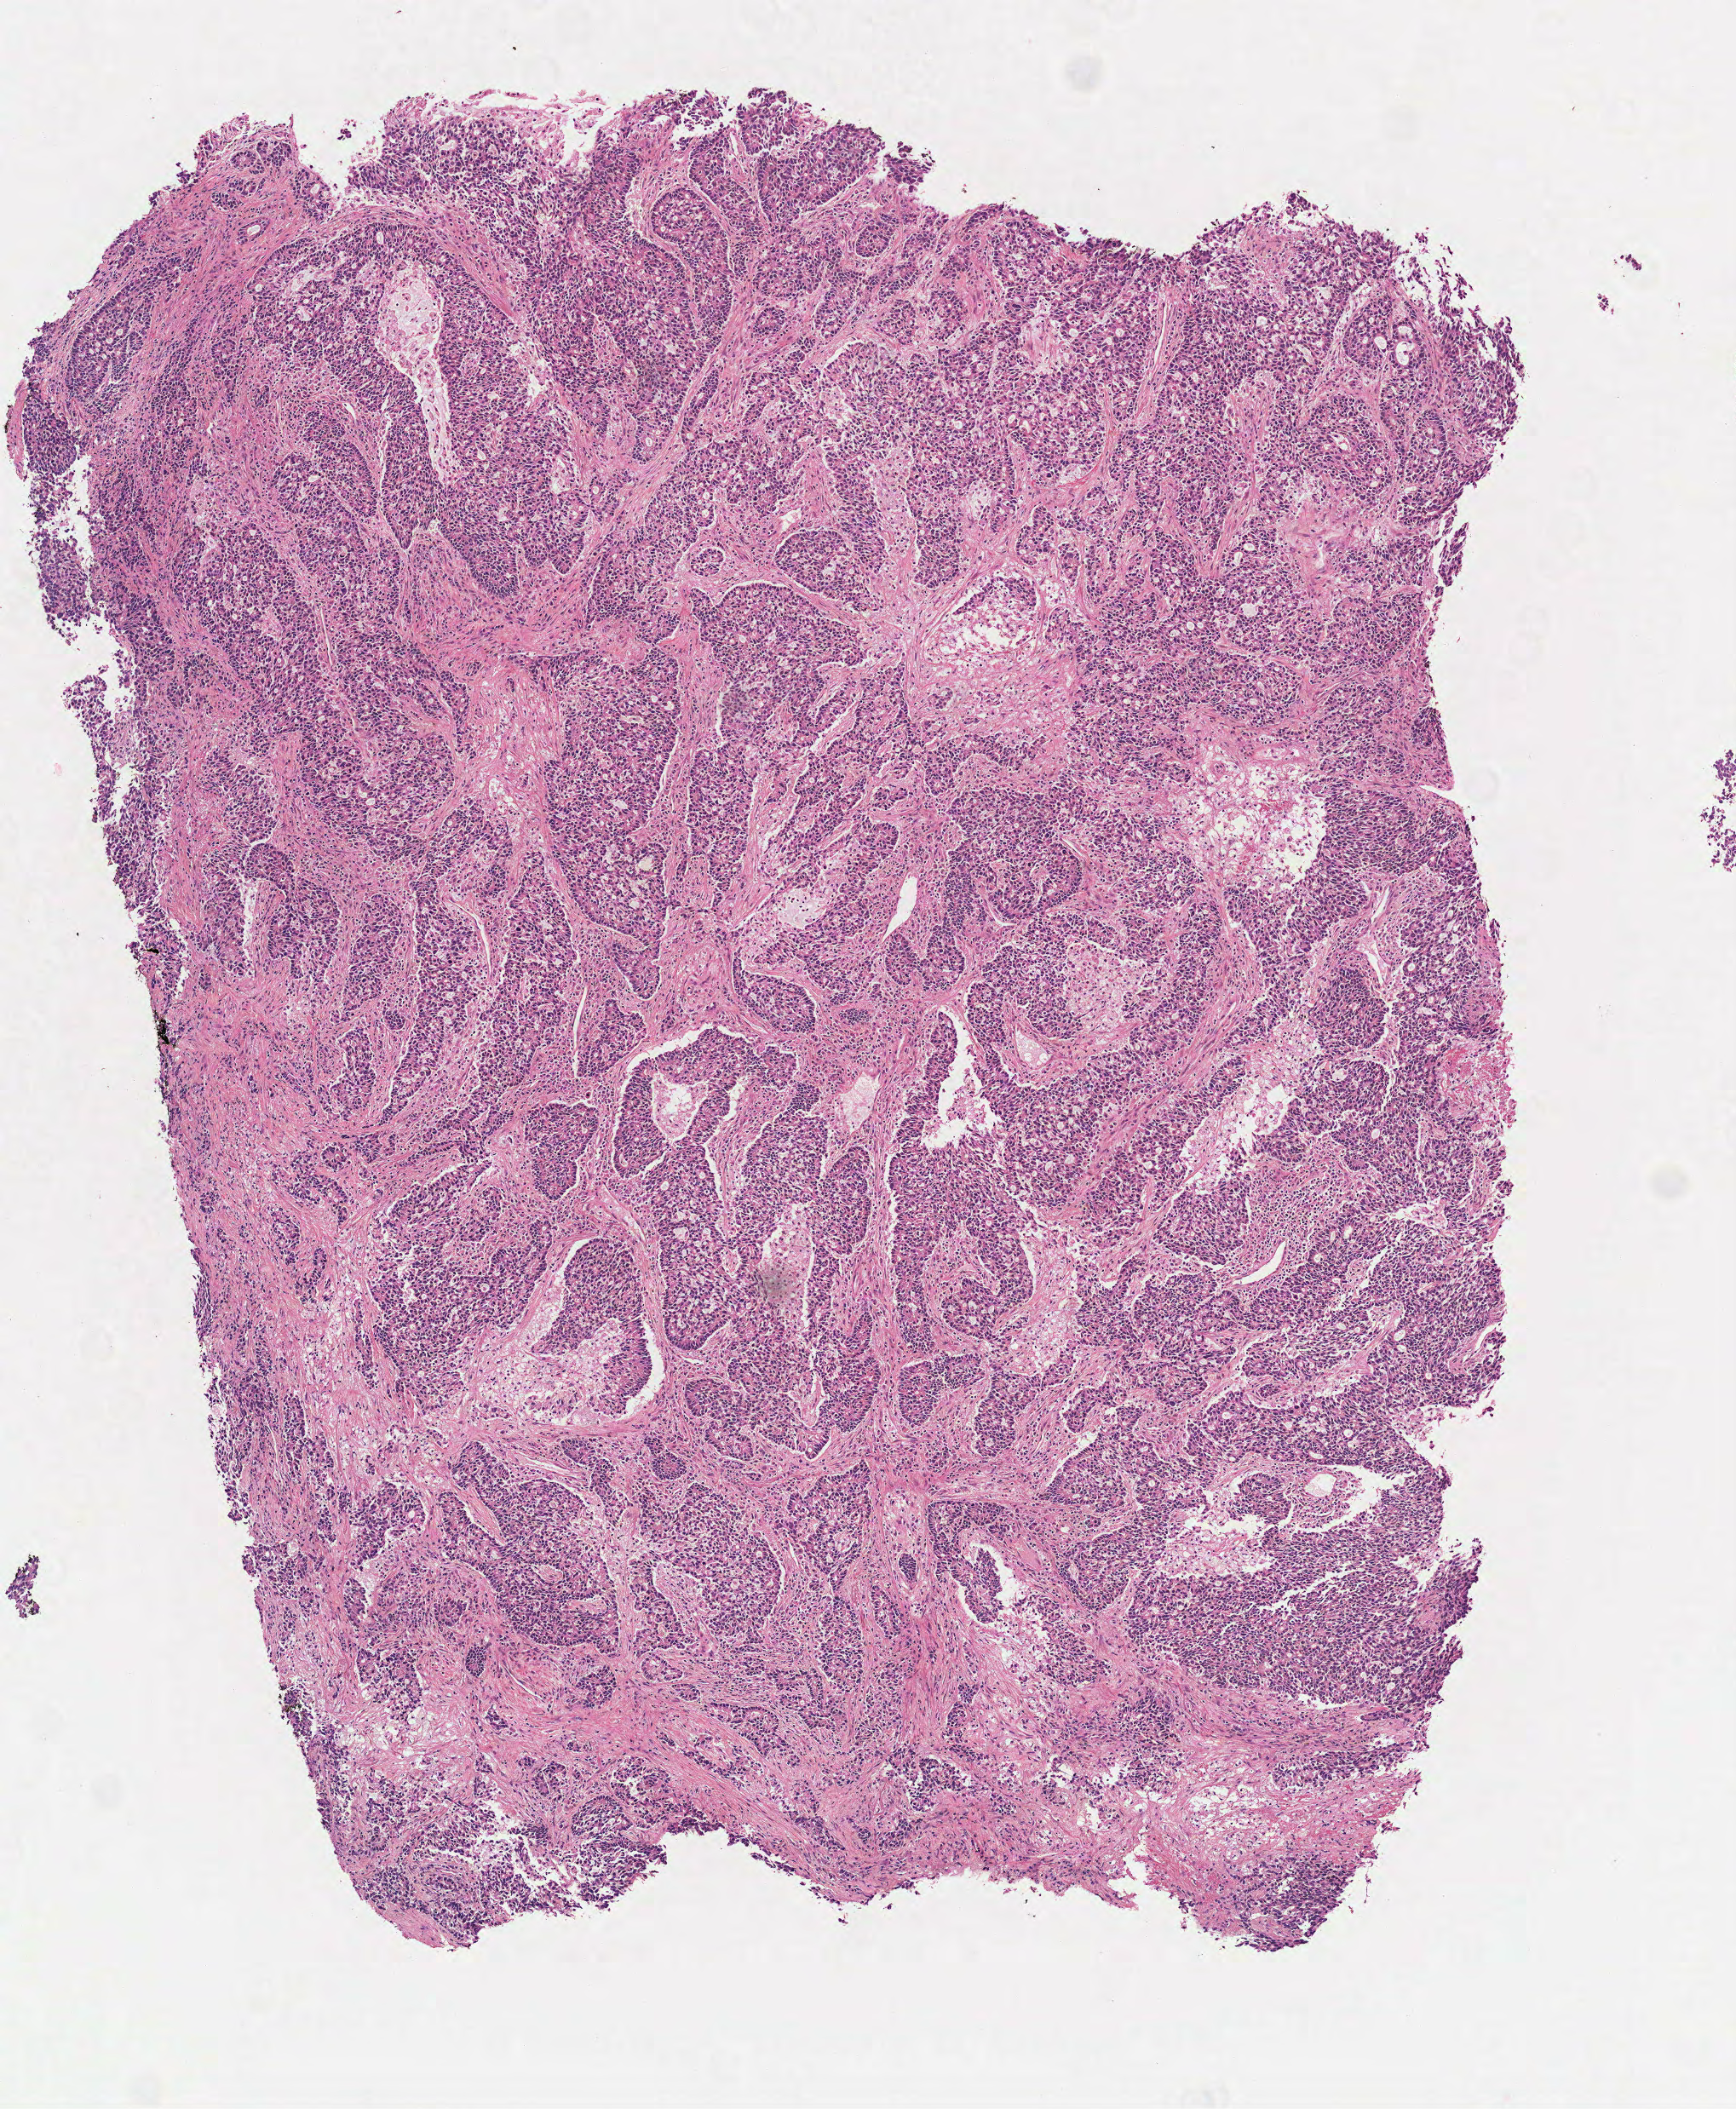
Digitized H&E-stained tissue section (whole slide), low-resolution overview of the scanned area, about 4.1 x 5.0 mm, frozen section from the top of the tissue portion, primary tumour sample from the lung. Patient: male, age at initial diagnosis 69 years. Composition of this section per pathologist review: tumour cells 100%, tumour nuclei 80%, normal cells 0%, stromal cells 0%, necrosis 0%. Infiltration values recorded for this section: lymphocyte infiltration 5%, monocyte infiltration 5%, neutrophil infiltration 2%.
Pathologic diagnosis: Adenocarcinoma, NOS (upper lobe, lung). AJCC pathologic stage: IIIA (6th edition).